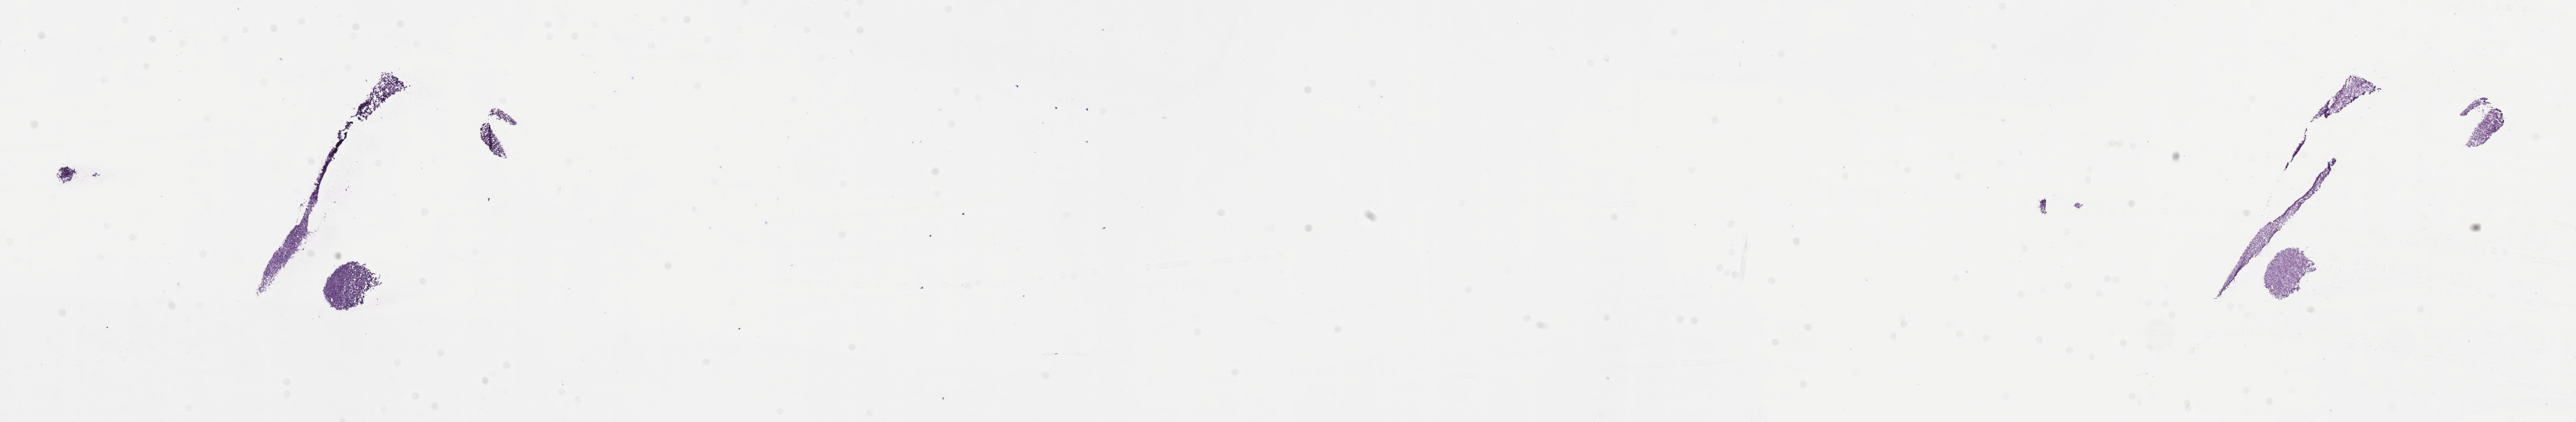
Whole-slide image, H&E stain of tumor tissue from the cerebellum — low-resolution overview of the scanned area, about 26.7 x 4.4 mm; frozen section. Patient female; age 186 months.
Recorded diagnosis: Medulloblastoma, NOS.